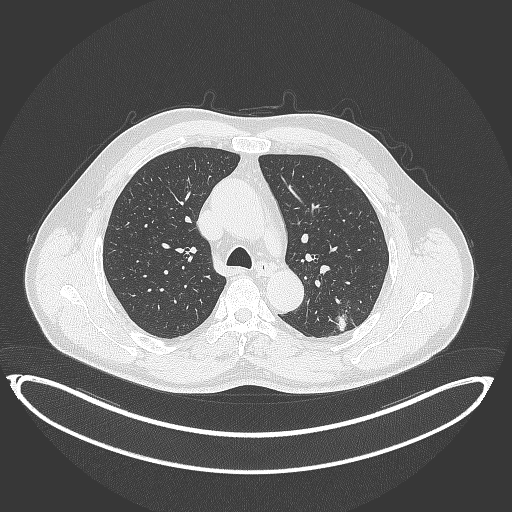
Chest CT, one axial slice; slice 244 of 399 in the series (ordered by position); reconstruction kernel B70f; lung window (W 1500 / L -600 HU); 1 mm slice thickness; 512 × 512 image matrix. Male patient, age 58 years. From the clinical record (not read from this slice): clinical TNM (as recorded): T1c N0 M0.
Outlined on this slice (bounding box drawn by a radiologist):
- lung tumour (recorded histology: adenocarcinoma): box from (x=330, y=307) to (x=354, y=336) px